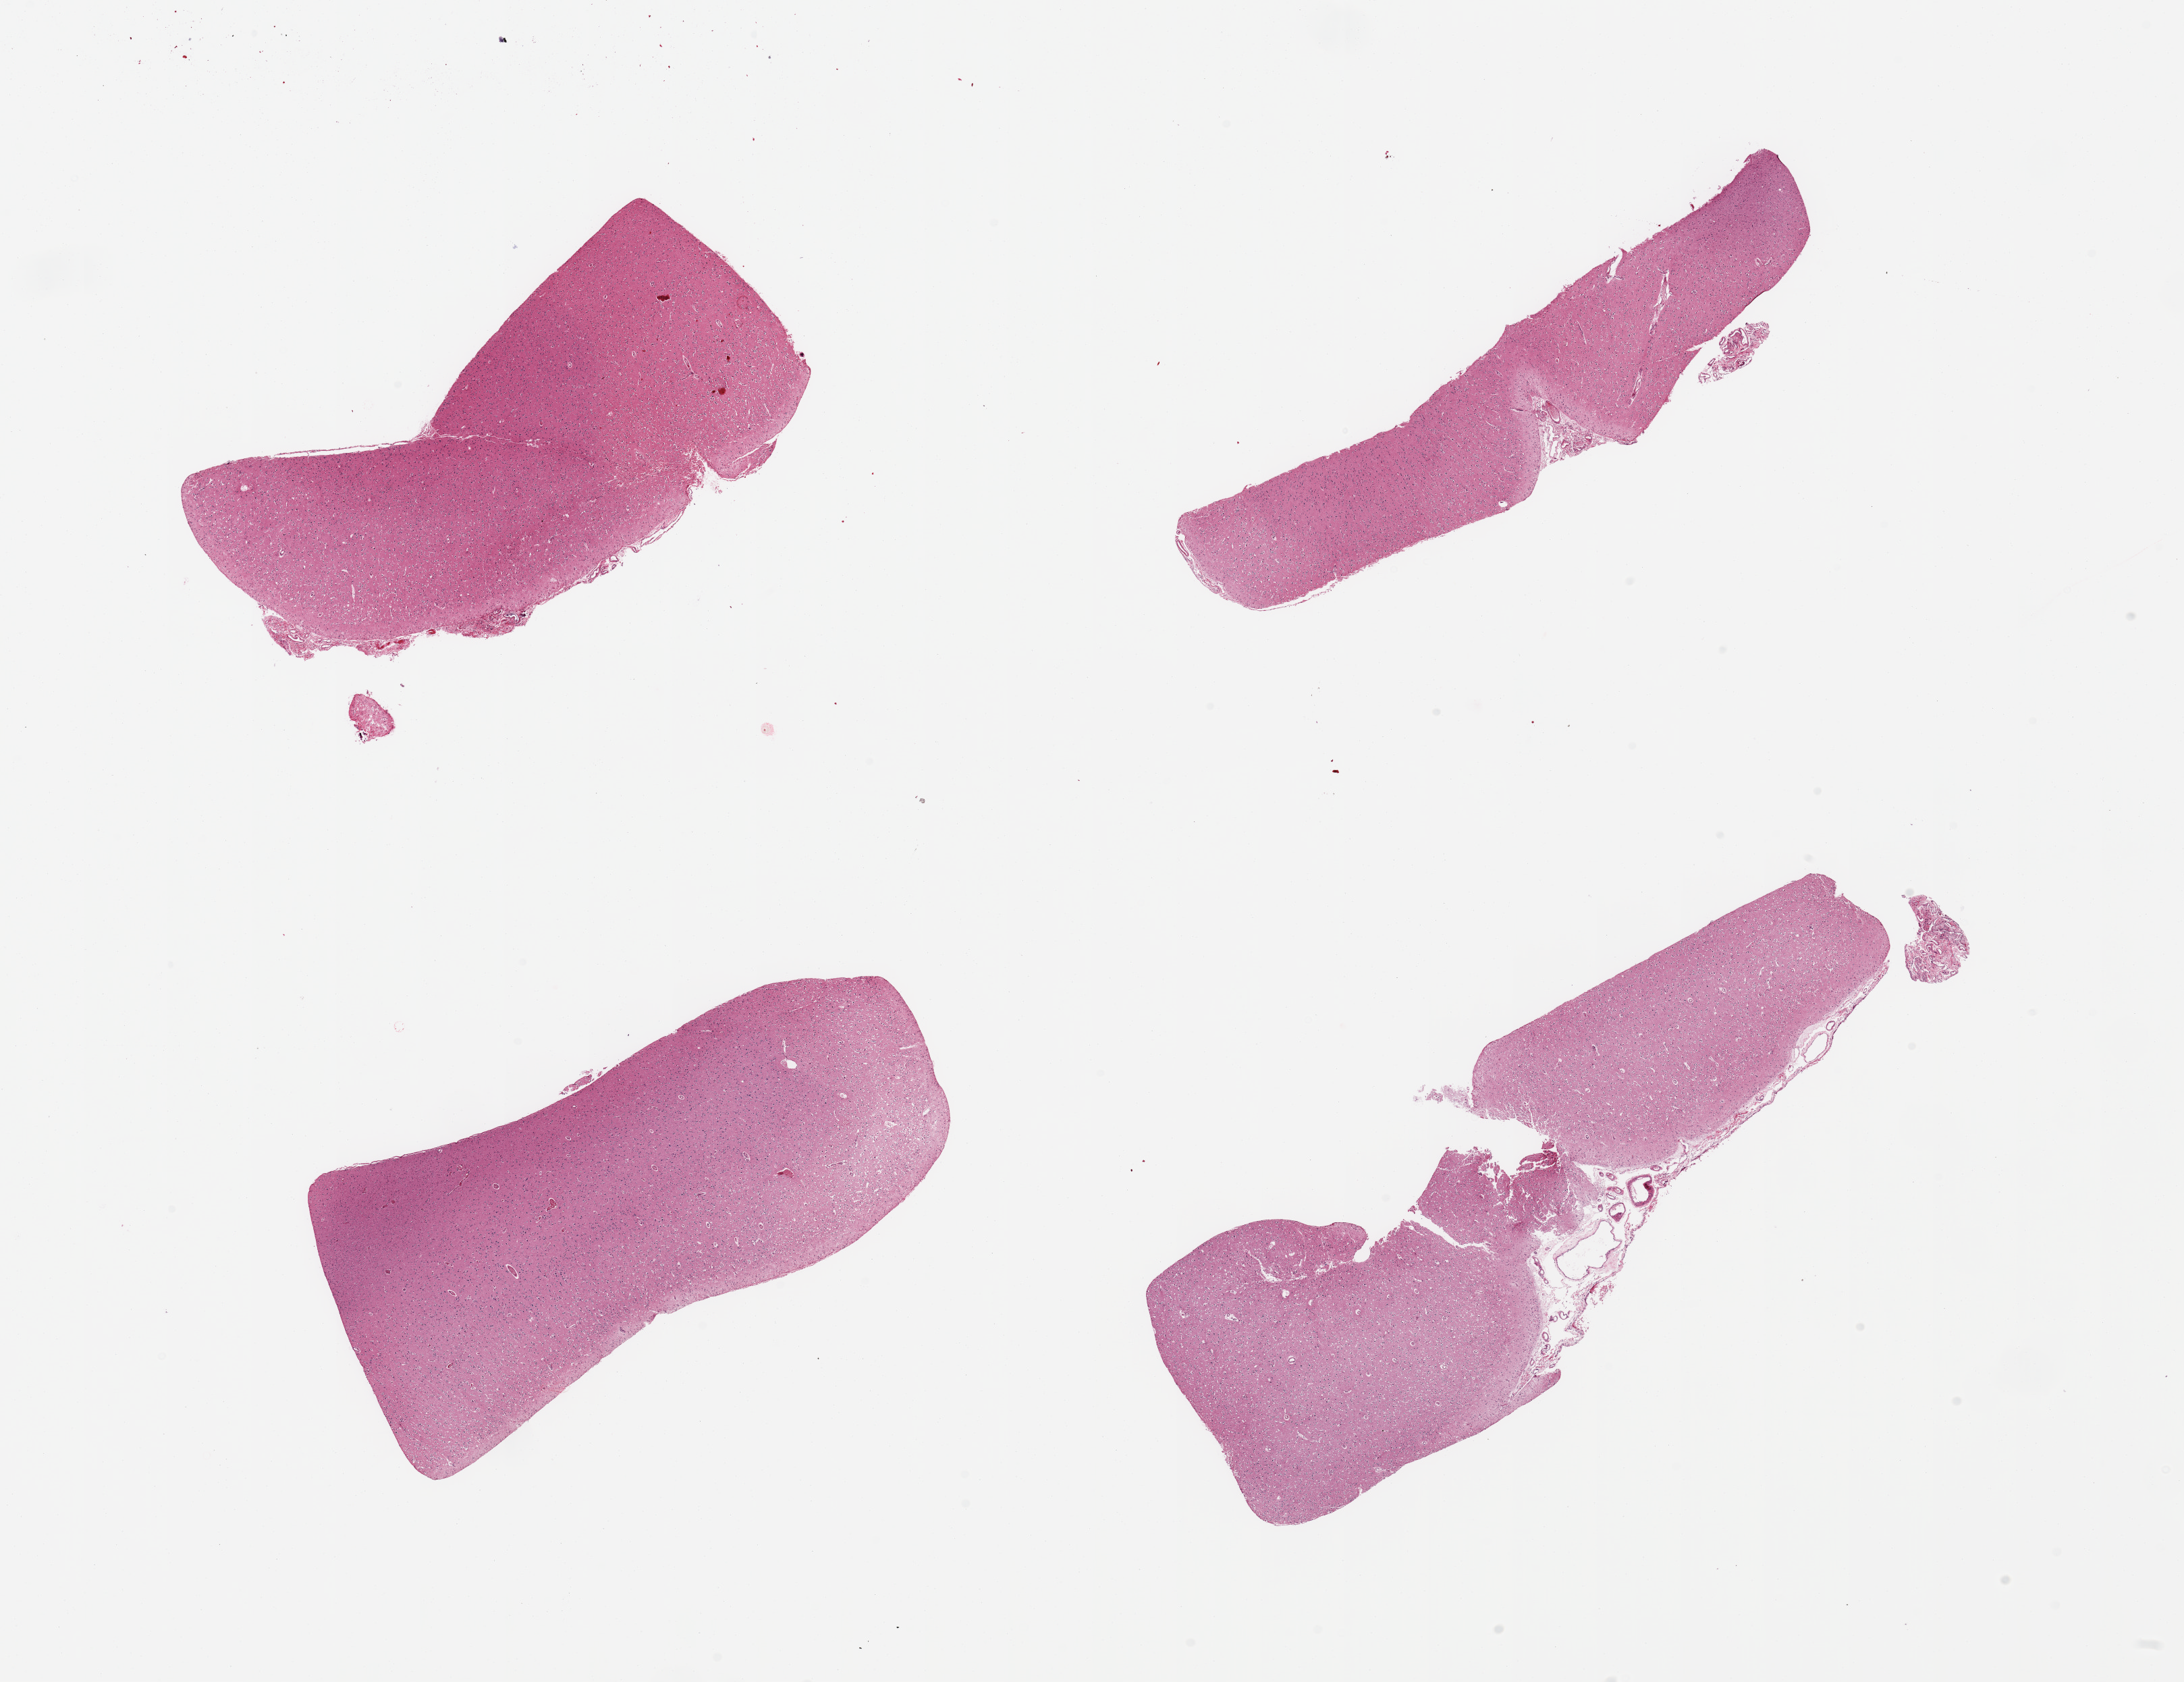
Digitized haematoxylin and eosin-stained section, brightfield — whole scanned area (about 25.6 x 19.7 mm) shown as a low-resolution overview, PAXgene-fixed, paraffin-embedded tissue, target tissue: cerebral cortex, donor tissue sample. Female donor.
Reviewer comment on this tissue sample: 4 pieces, no abnormalities.